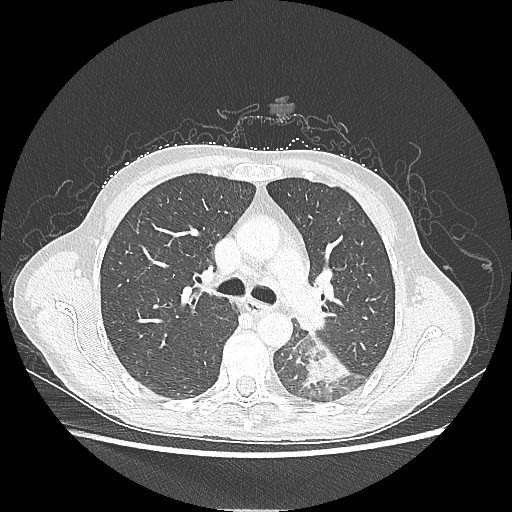
Chest CT, one axial slice; slice 140 of 220 in the series (ordered by position); reconstruction kernel LUNG; lung window (W 1500 / L -600 HU); 512 × 512 image matrix, field of view 360 × 360 mm. Patient: female, 53 years. Case-level facts recorded for this patient, not image findings: clinical TNM (as recorded): T3 N0 M0.
Outlined on this slice (rectangle marked by the reading radiologist):
- lung tumour (recorded histology: adenocarcinoma): box from (x=296, y=341) to (x=354, y=393) px